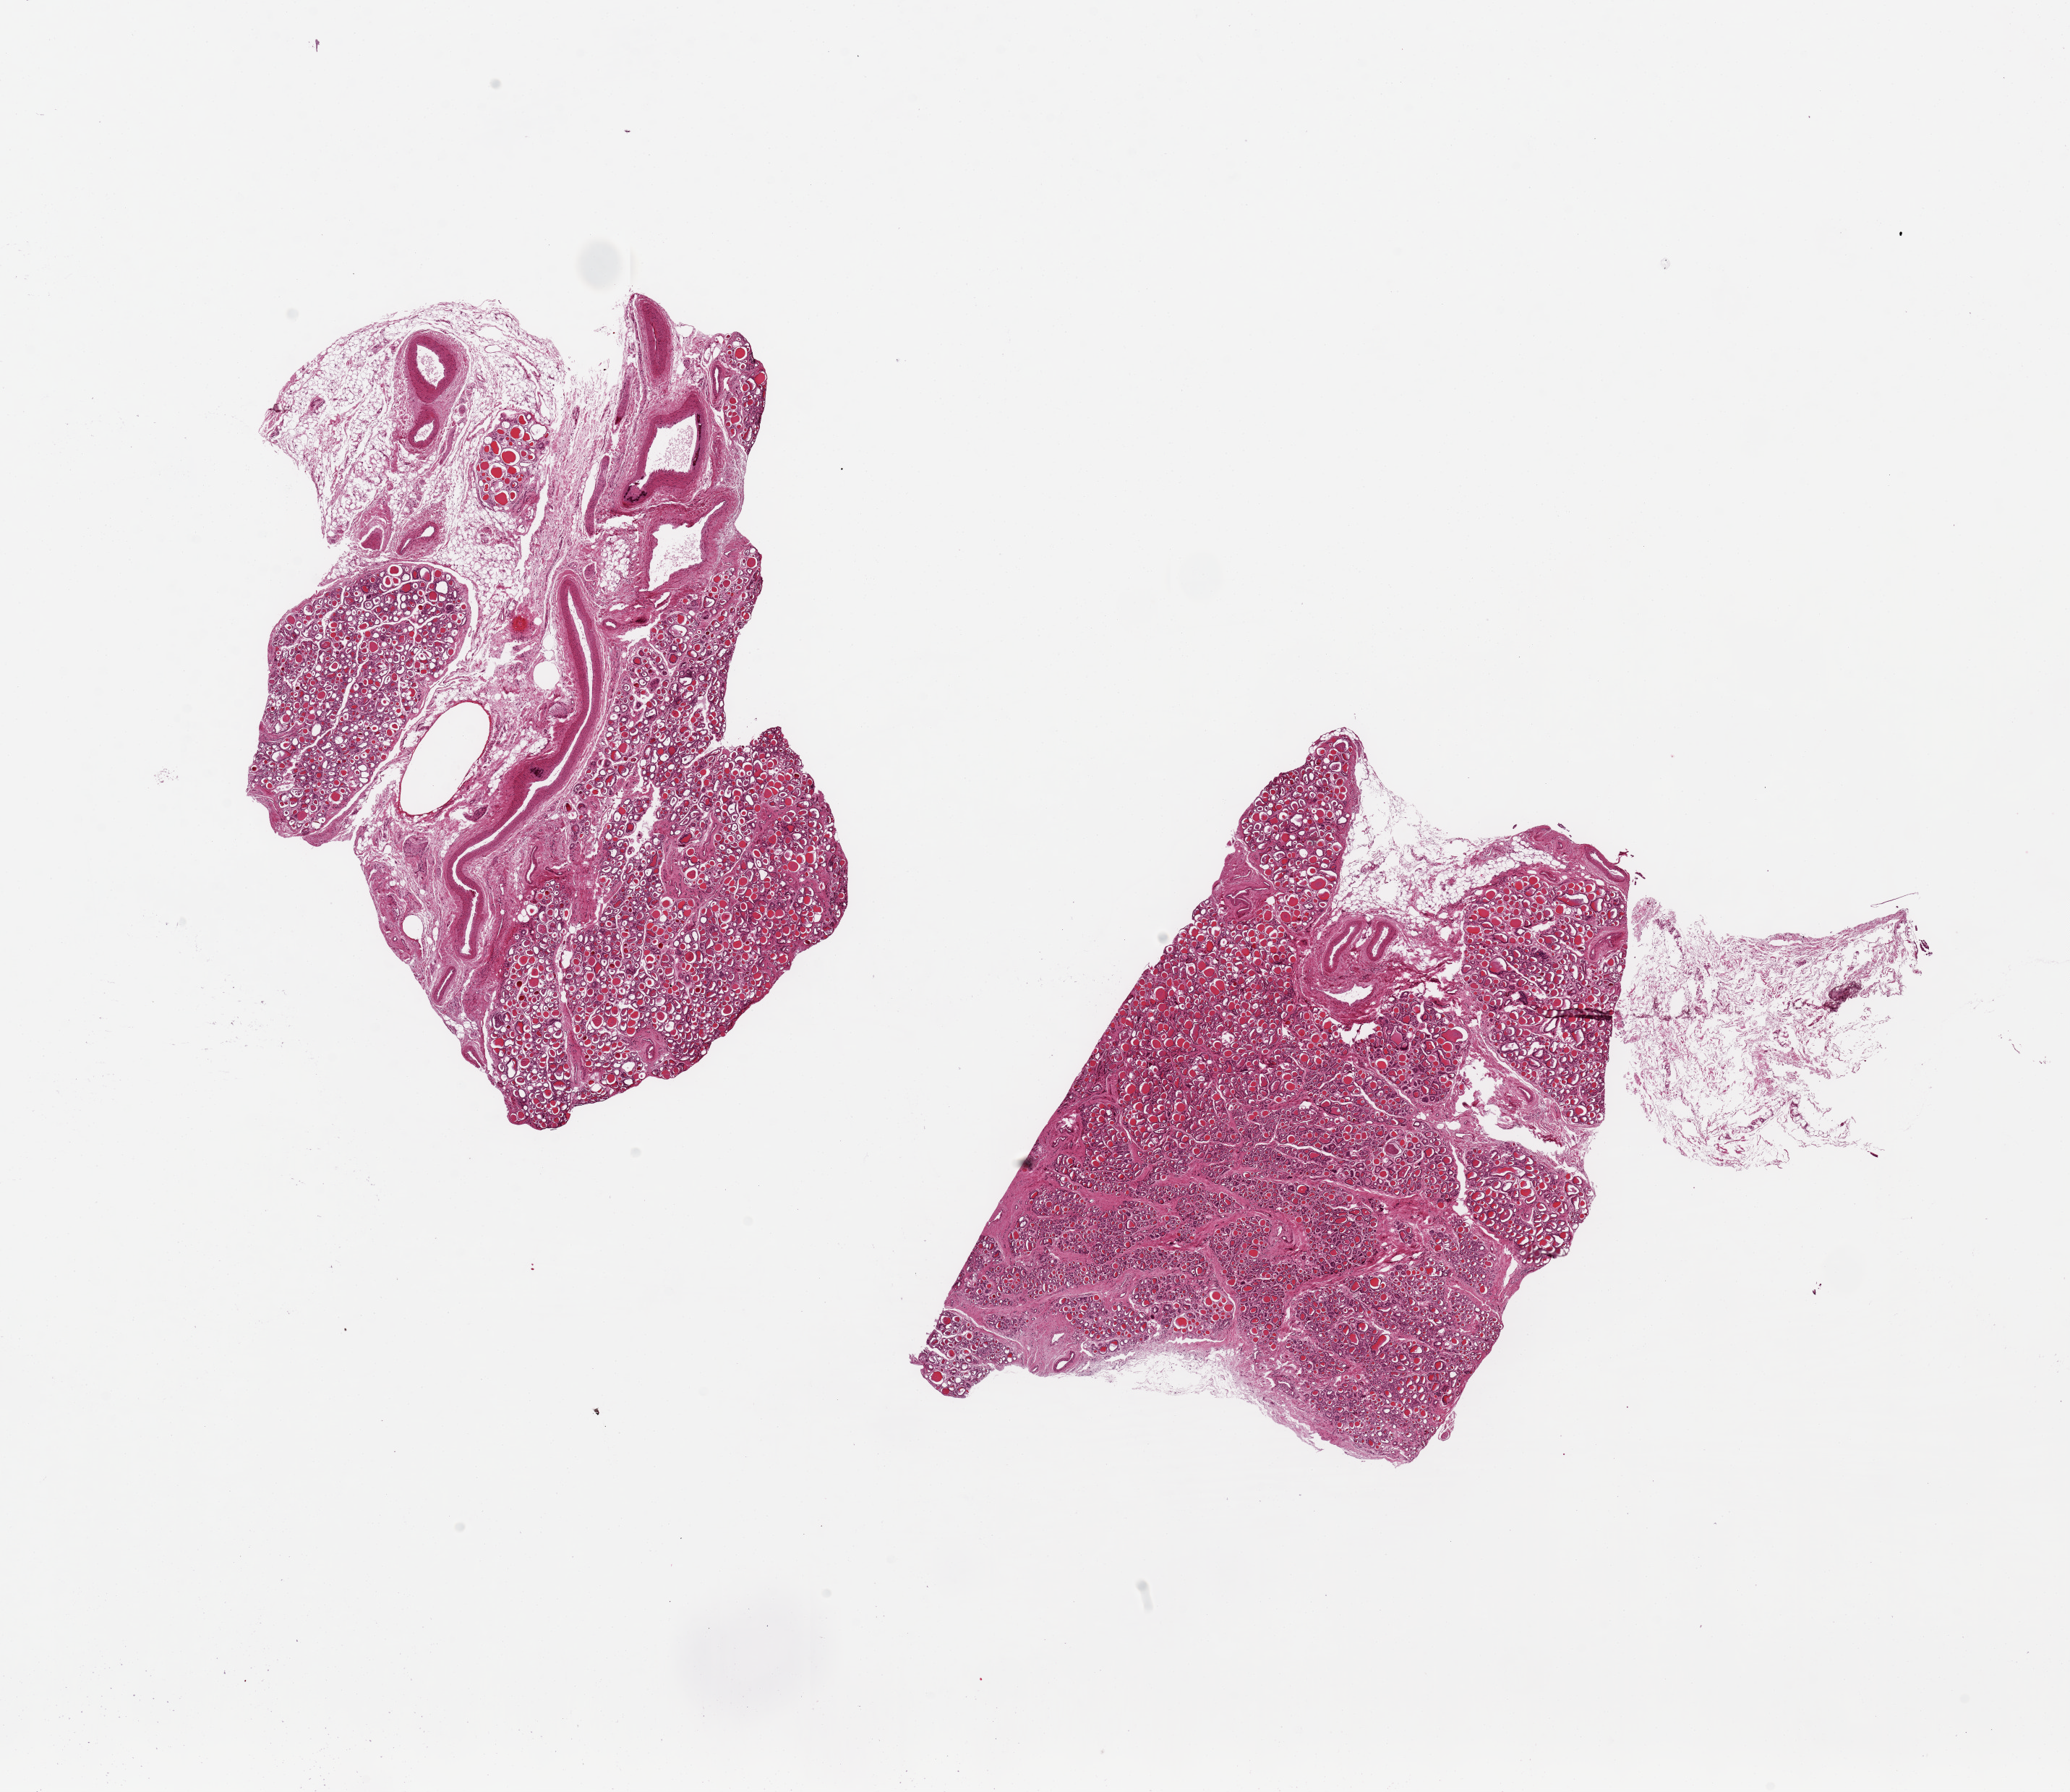
Digitized hematoxylin and eosin (H&E)-stained section, a low-resolution overview of the entire scanned area, about 22.6 x 19.6 mm (acquisition: 20x scan). PAXgene-fixed paraffin-embedded (PFPE) section. Target tissue: thyroid. Donor tissue sample. Donor sex: female.
Review note (as recorded): 2 pieces, 9x7 & 8x8mm; 20% external adipose.